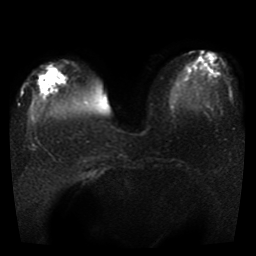
Breast MRI, one axial slice. Position 10 of 41 along the scan axis. Diffusion-weighted series; image 2 of 4 stored at this slice position (different b-values; order by instance number). 1.5 T. 5 mm slice thickness. 256 × 256 image matrix. Female patient.
Outlined on this slice (manually delineated by an expert):
- tumour on diffusion-weighted imaging: box from (x=39, y=72) to (x=54, y=91) px